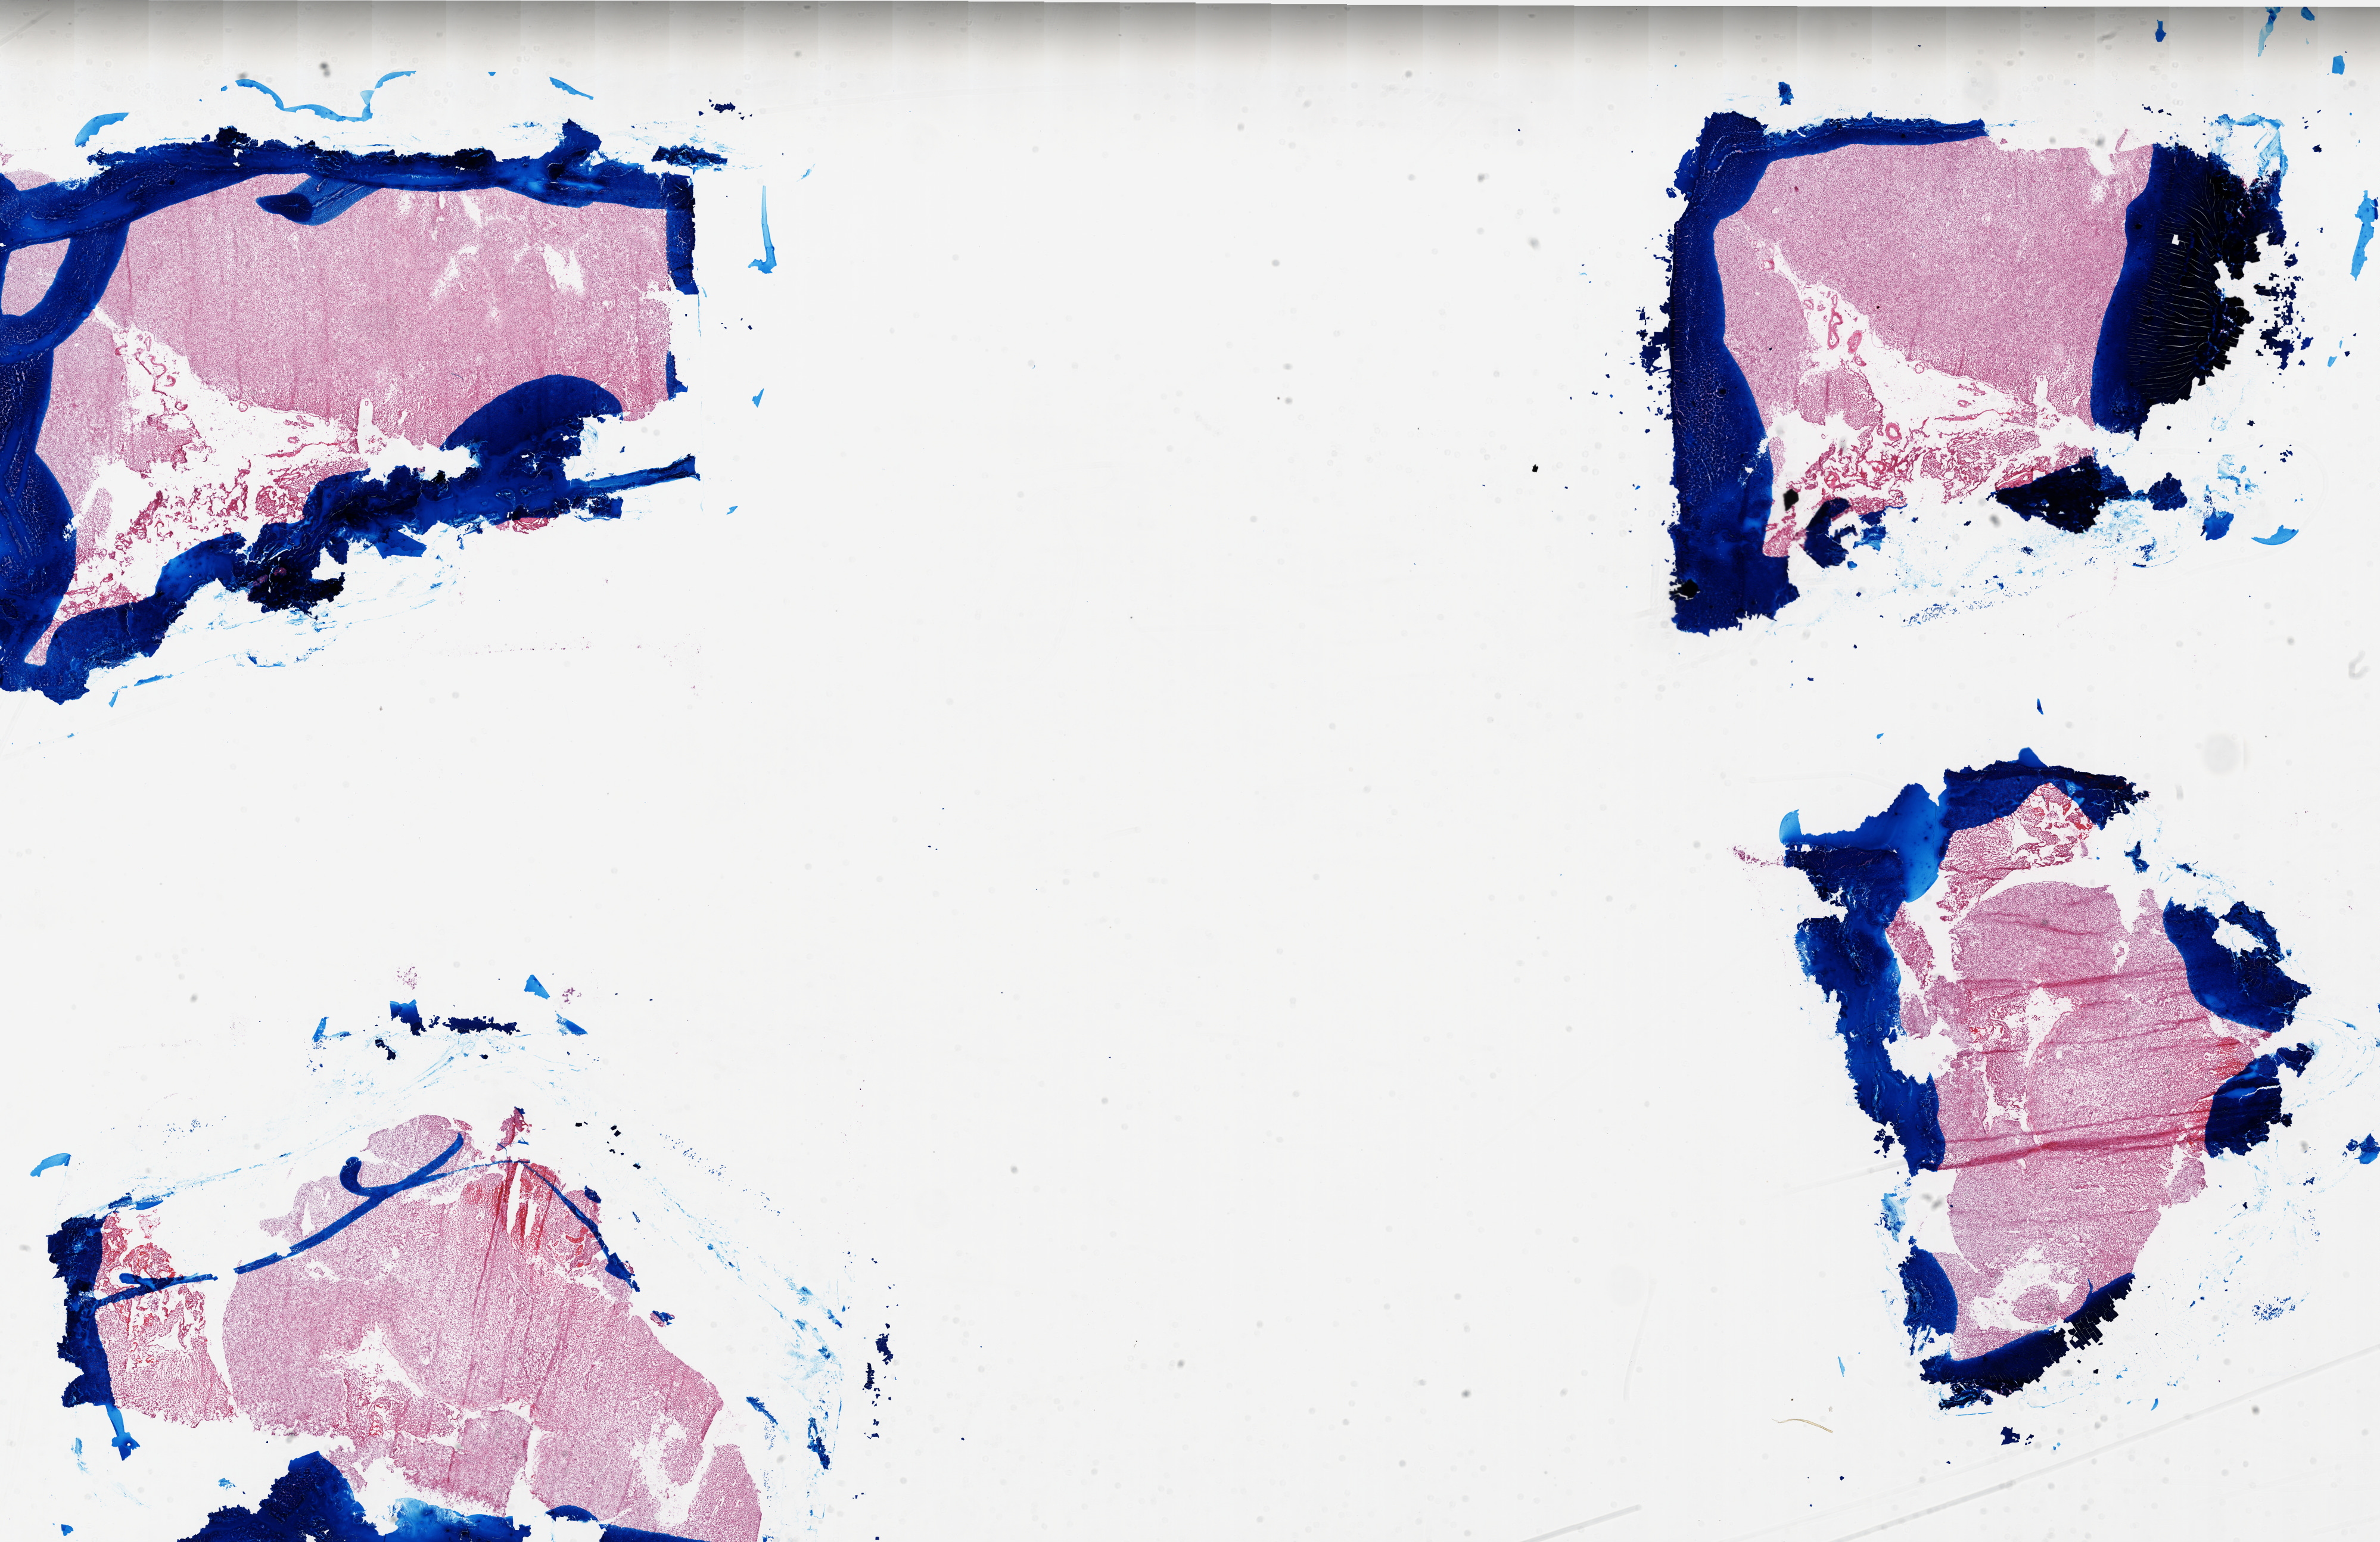
Digitized Hematoxylin and eosin (H&E) stained tissue section (whole slide) — shown as a low-resolution overview of the whole scanned area (about 32.0 x 20.7 mm, from a 20x scan). Frozen section from the top of the tissue portion. Primary tumour sample from the brain. Female patient; age at initial diagnosis 38 years. Pathologist review of this section (percent, as recorded): tumour cells 100%, tumour nuclei 100%, normal cells 0%, stromal cells 0%, necrosis 0%.
Histologic diagnosis: Glioblastoma.